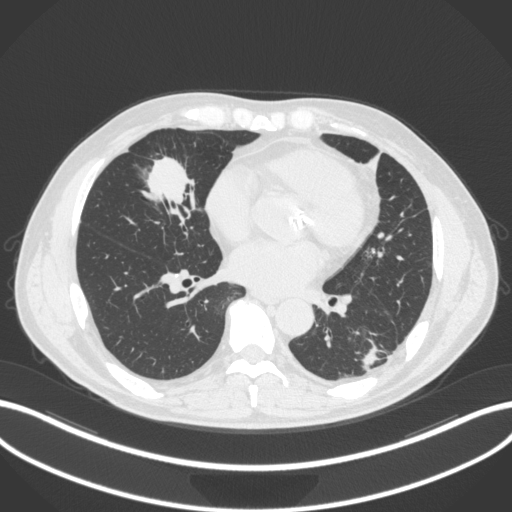
Chest CT, one axial slice; slice 123 of 399 in the series (ordered by position); reconstruction kernel B31f; 120 kVp; lung window (W 1500 / L -600 HU); 1 mm slice thickness; 512 × 512 image matrix, field of view 400 × 400 mm. Male patient, age 59 years. Case-level facts recorded for this patient, not image findings: clinical TNM (as recorded): T2a N1 M0.
Outlined on this slice (bounding box drawn by a radiologist):
- lung tumour (recorded histology: adenocarcinoma): bounding box (x1, y1, x2, y2) in pixels: (137, 148, 200, 217)